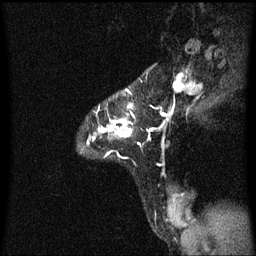
Breast MRI (dynamic contrast-enhanced), one sagittal slice; slice 48 of 60 in the series (ordered by position); dynamic contrast-enhanced series, image 2 of 3 at this slice position (ordered by acquisition); 1.5 T; TE 4.2 ms, TR 8.4 ms; 256 × 256 image matrix, field of view 200 × 200 mm. Female patient, age 32 years.
Structures marked on this image (semi-automatically segmented with operator editing):
- analysis volume of interest (the breast-tissue region the enhancement analysis was run in; not a lesion): bounding box (x1, y1, x2, y2) in pixels: (88, 78, 141, 145)
- tumour enhancement mask (voxels above the 70 % enhancement threshold inside the analysis volume of interest): (88, 90, 133, 145)